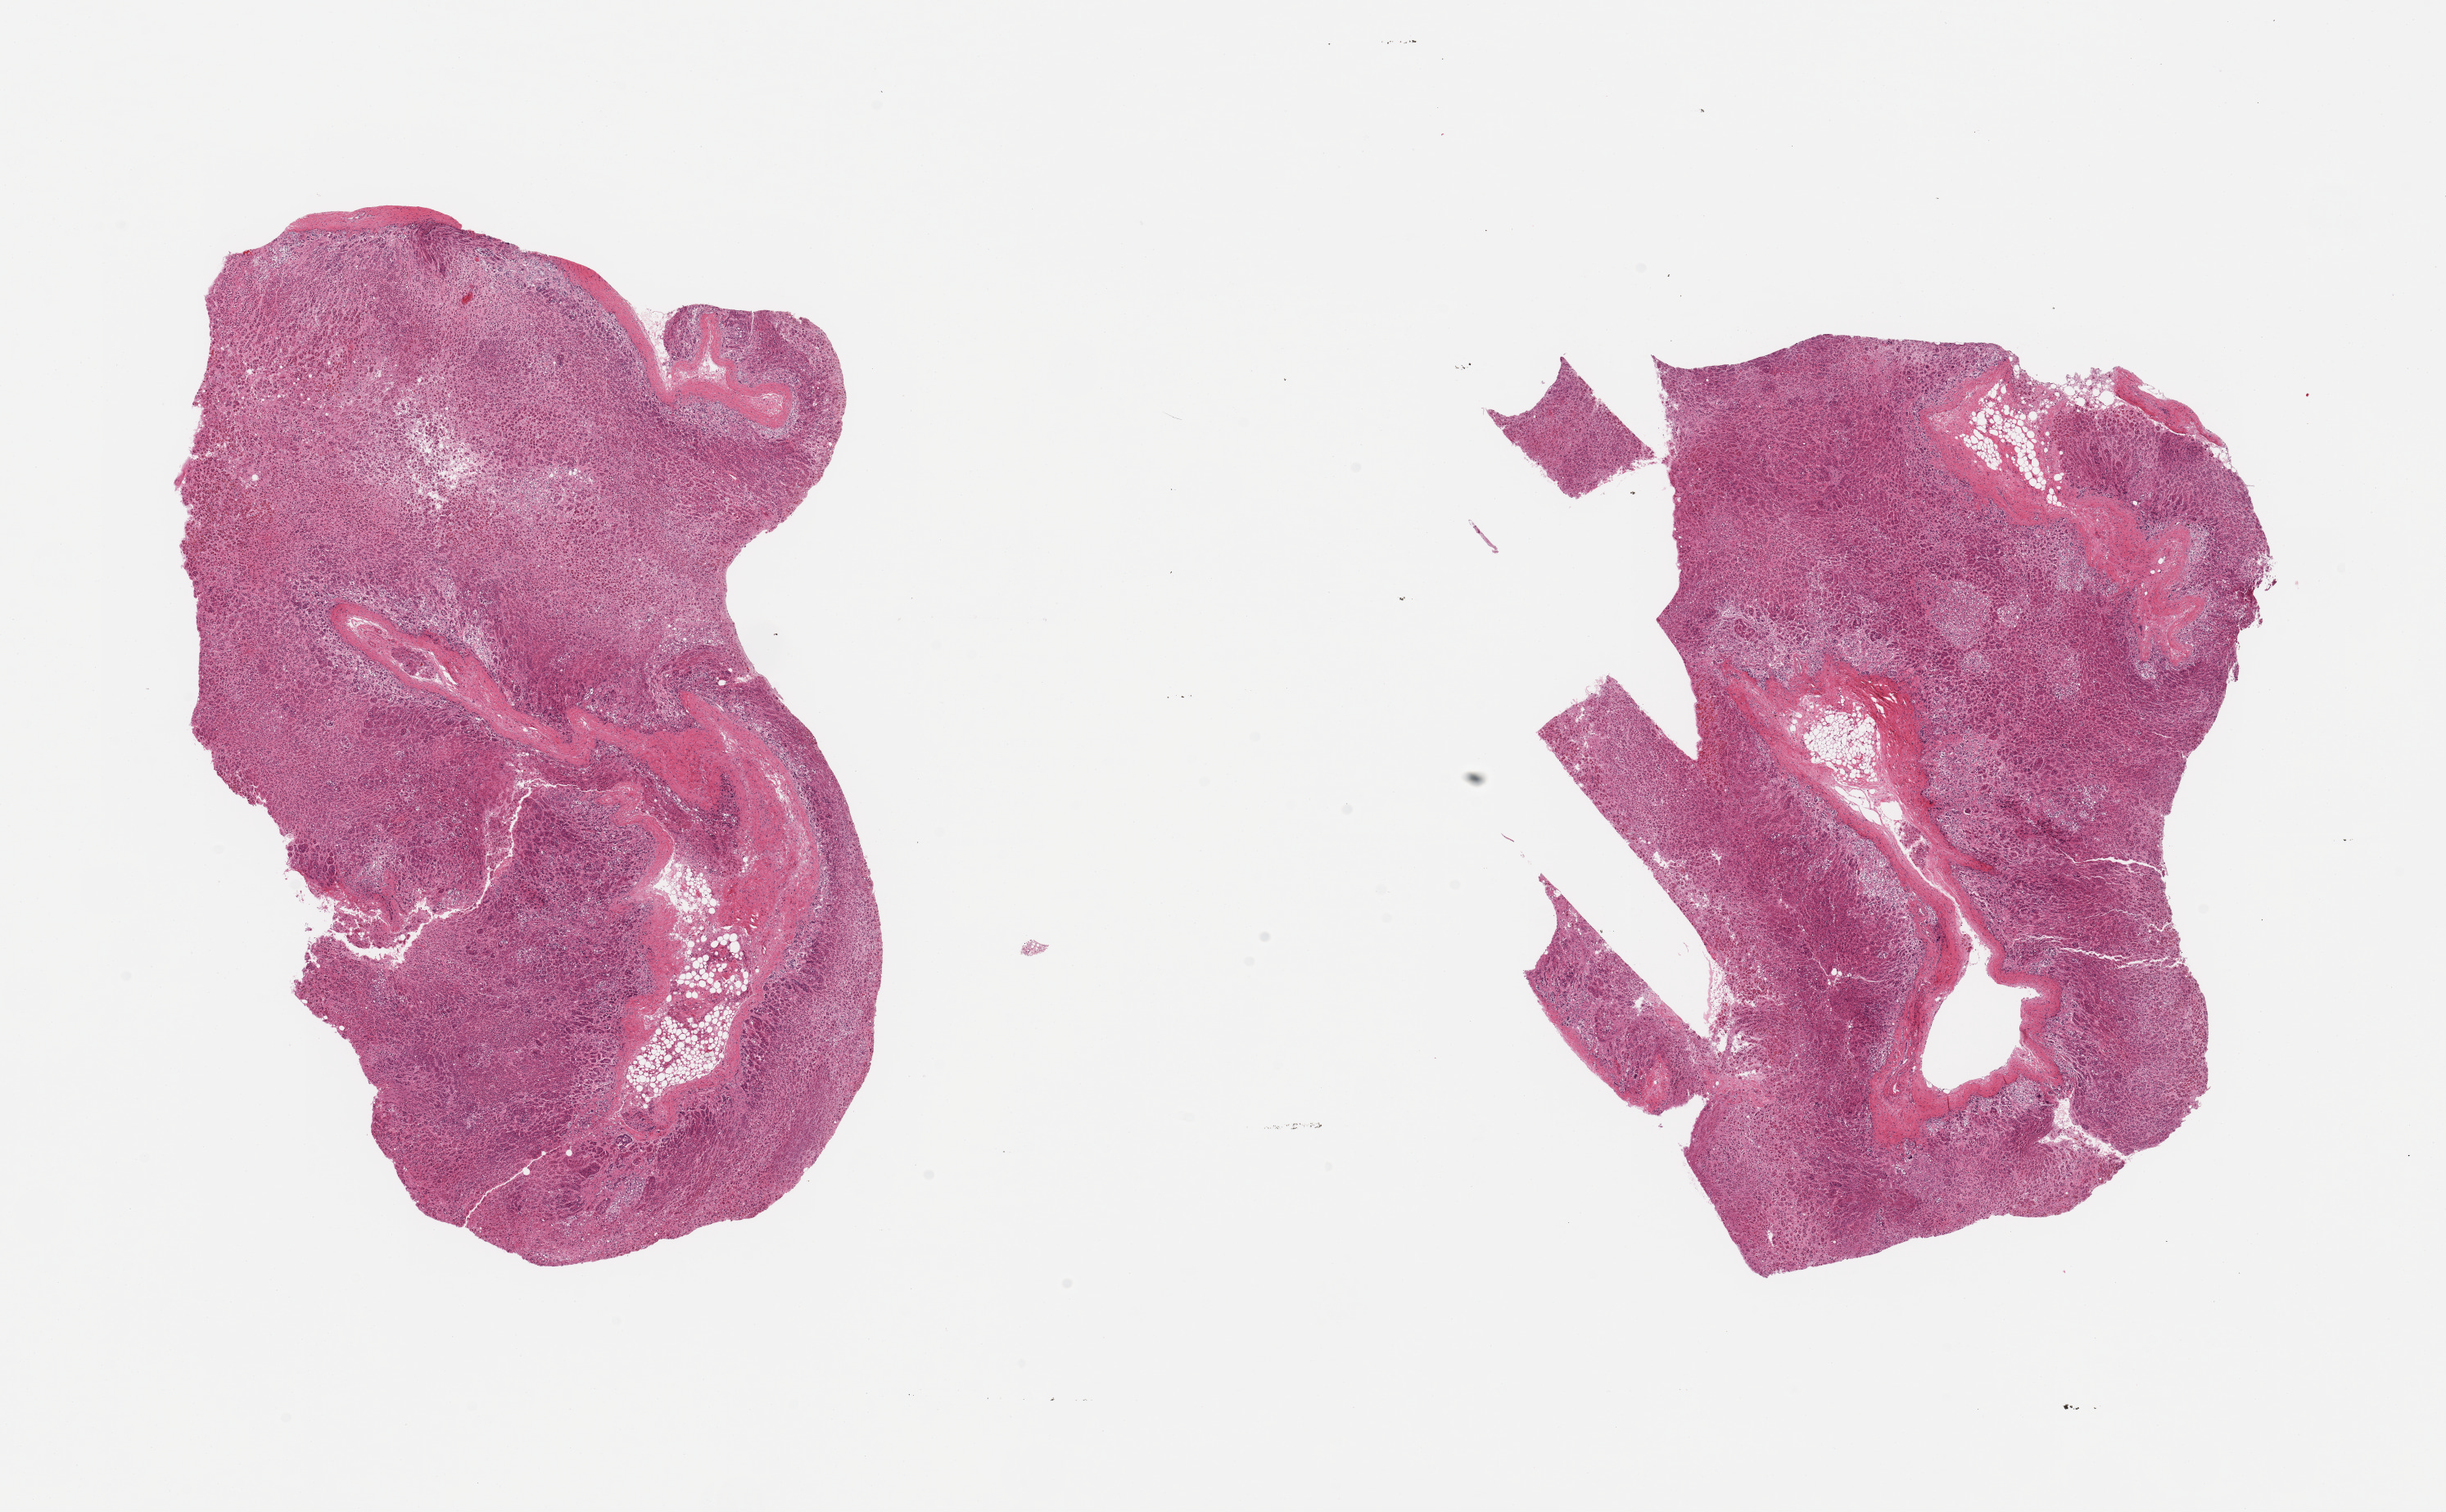
Haematoxylin and eosin whole-slide image — whole scanned area (about 23.6 x 14.6 mm, slide scanned at 20x) shown as a low-resolution overview, PAXgene-fixed paraffin-embedded (PFPE) section, section of adrenal gland (target tissue), tissue donor sample. Donor: male.
- pathologist's review note for this sample: 2 pieces, cortex, ~5% adherent/interstitial fat